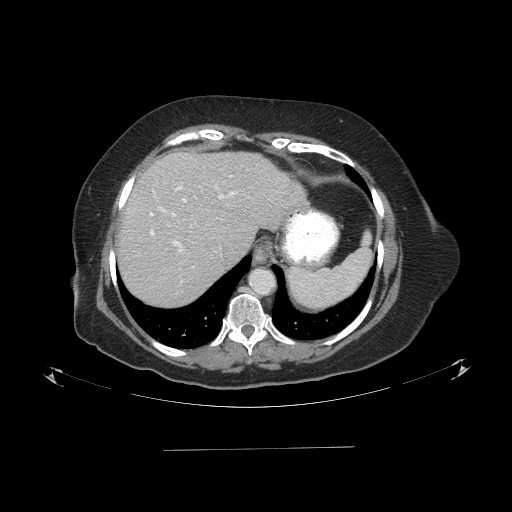
Contrast-enhanced abdominal CT (liver protocol), one axial slice. Position 71 of 103 along the scan axis. 120 kVp. One of 2 acquisitions stored at this slice position. Soft-tissue window (W 400 / L 40 HU). 2.5 mm slice thickness. 512 × 512 image matrix. Case-level facts recorded for this patient, not image findings: diagnosis: hepatocellular carcinoma (patient treated with transarterial chemoembolisation; whether this scan precedes or follows treatment is not stated here); TNM stage (as recorded): Stage-IIIA; Child-Pugh class: A; tumour differentiation: poorly differentiated; tumour nodularity: multinodular.
Structures marked on this image (semi-automatic segmentation, software-assisted and operator-edited):
- liver parenchyma outside the tumour (the mass and vessels are separate outlines, so this box may not span the whole liver): bounding box (x1, y1, x2, y2) in pixels: (116, 152, 306, 304)
- liver vessels: (150, 175, 236, 252)